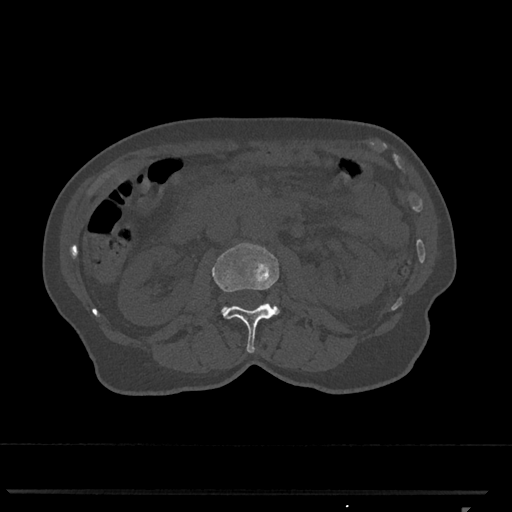
CT including the spine, one axial slice. Position 325 of 793 along the scan axis. 120 kVp. Bone window (W 1800 / L 400 HU). 512 × 512 image matrix, field of view 380 × 380 mm. Patient: female, 62 years. From the clinical record (not read from this slice): primary cancer: renal.
Annotated regions visible in this slice (semi-automatic segmentation, software-assisted and operator-edited):
- L2 vertebra: bounding box (x1, y1, x2, y2) in pixels: (212, 243, 280, 353)